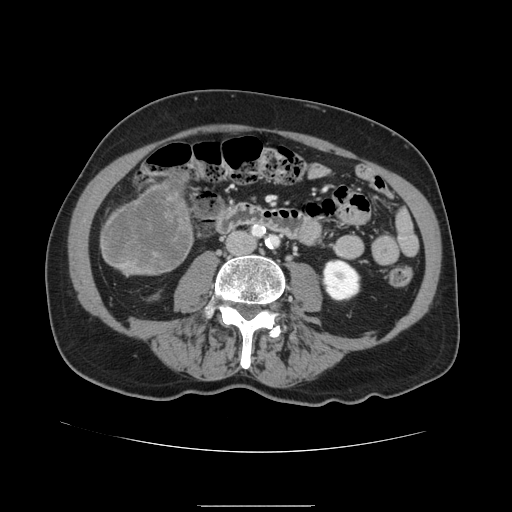
Contrast-enhanced abdominal CT, one axial slice; slice 24 of 168 in the series (ordered by position); intravenous contrast given; soft-tissue window (W 400 / L 40 HU); 512 × 512 image matrix, field of view 386 × 386 mm. Male patient, age 74 years. From the clinical record (not read from this slice): diagnosis: colorectal cancer liver metastases, imaged before liver resection; multiple liver metastases: no; largest metastasis: 14.5 cm.
Structures marked on this image (expert manual segmentation):
- liver: bounding box (x1, y1, x2, y2) in pixels: (101, 173, 193, 276)
- liver metastasis: (105, 176, 190, 271)